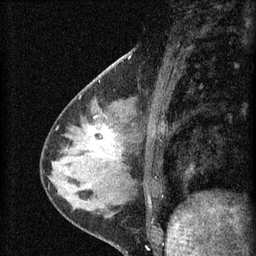
Breast MRI (dynamic contrast-enhanced), one sagittal slice; dynamic contrast-enhanced series, image 2 of 4 at this slice position (ordered by acquisition); 1.5 T; TE 4.2 ms, TR 8.2 ms; 2 mm slice thickness; 256 × 256 image matrix, field of view 180 × 180 mm. Female patient, age 37 years.
Outlined on this slice (semi-automatically segmented with operator editing):
- analysis volume of interest (the breast-tissue region the enhancement analysis was run in; not a lesion): bounding box (x1, y1, x2, y2) in pixels: (77, 116, 127, 175)
- tumour enhancement mask (voxels above the 70 % enhancement threshold inside the analysis volume of interest): (88, 125, 113, 143)